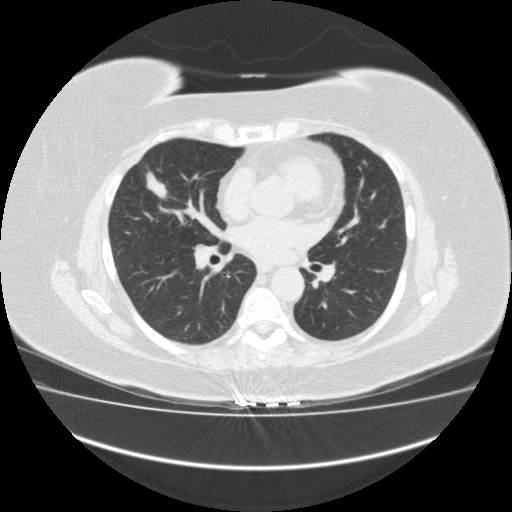
Low-dose screening chest CT, one axial slice. Slice 86 of 162 in the series (ordered by position). Lung window (W 1500 / L -600 HU). 2 mm slice thickness. 512 × 512 image matrix, field of view 420 × 420 mm.
Outlined on this slice (expert manual segmentation):
- lesion 1 (tumor, middle lobe of right lung): bounding box <146,172,167,199> (left, top, right, bottom; pixels)